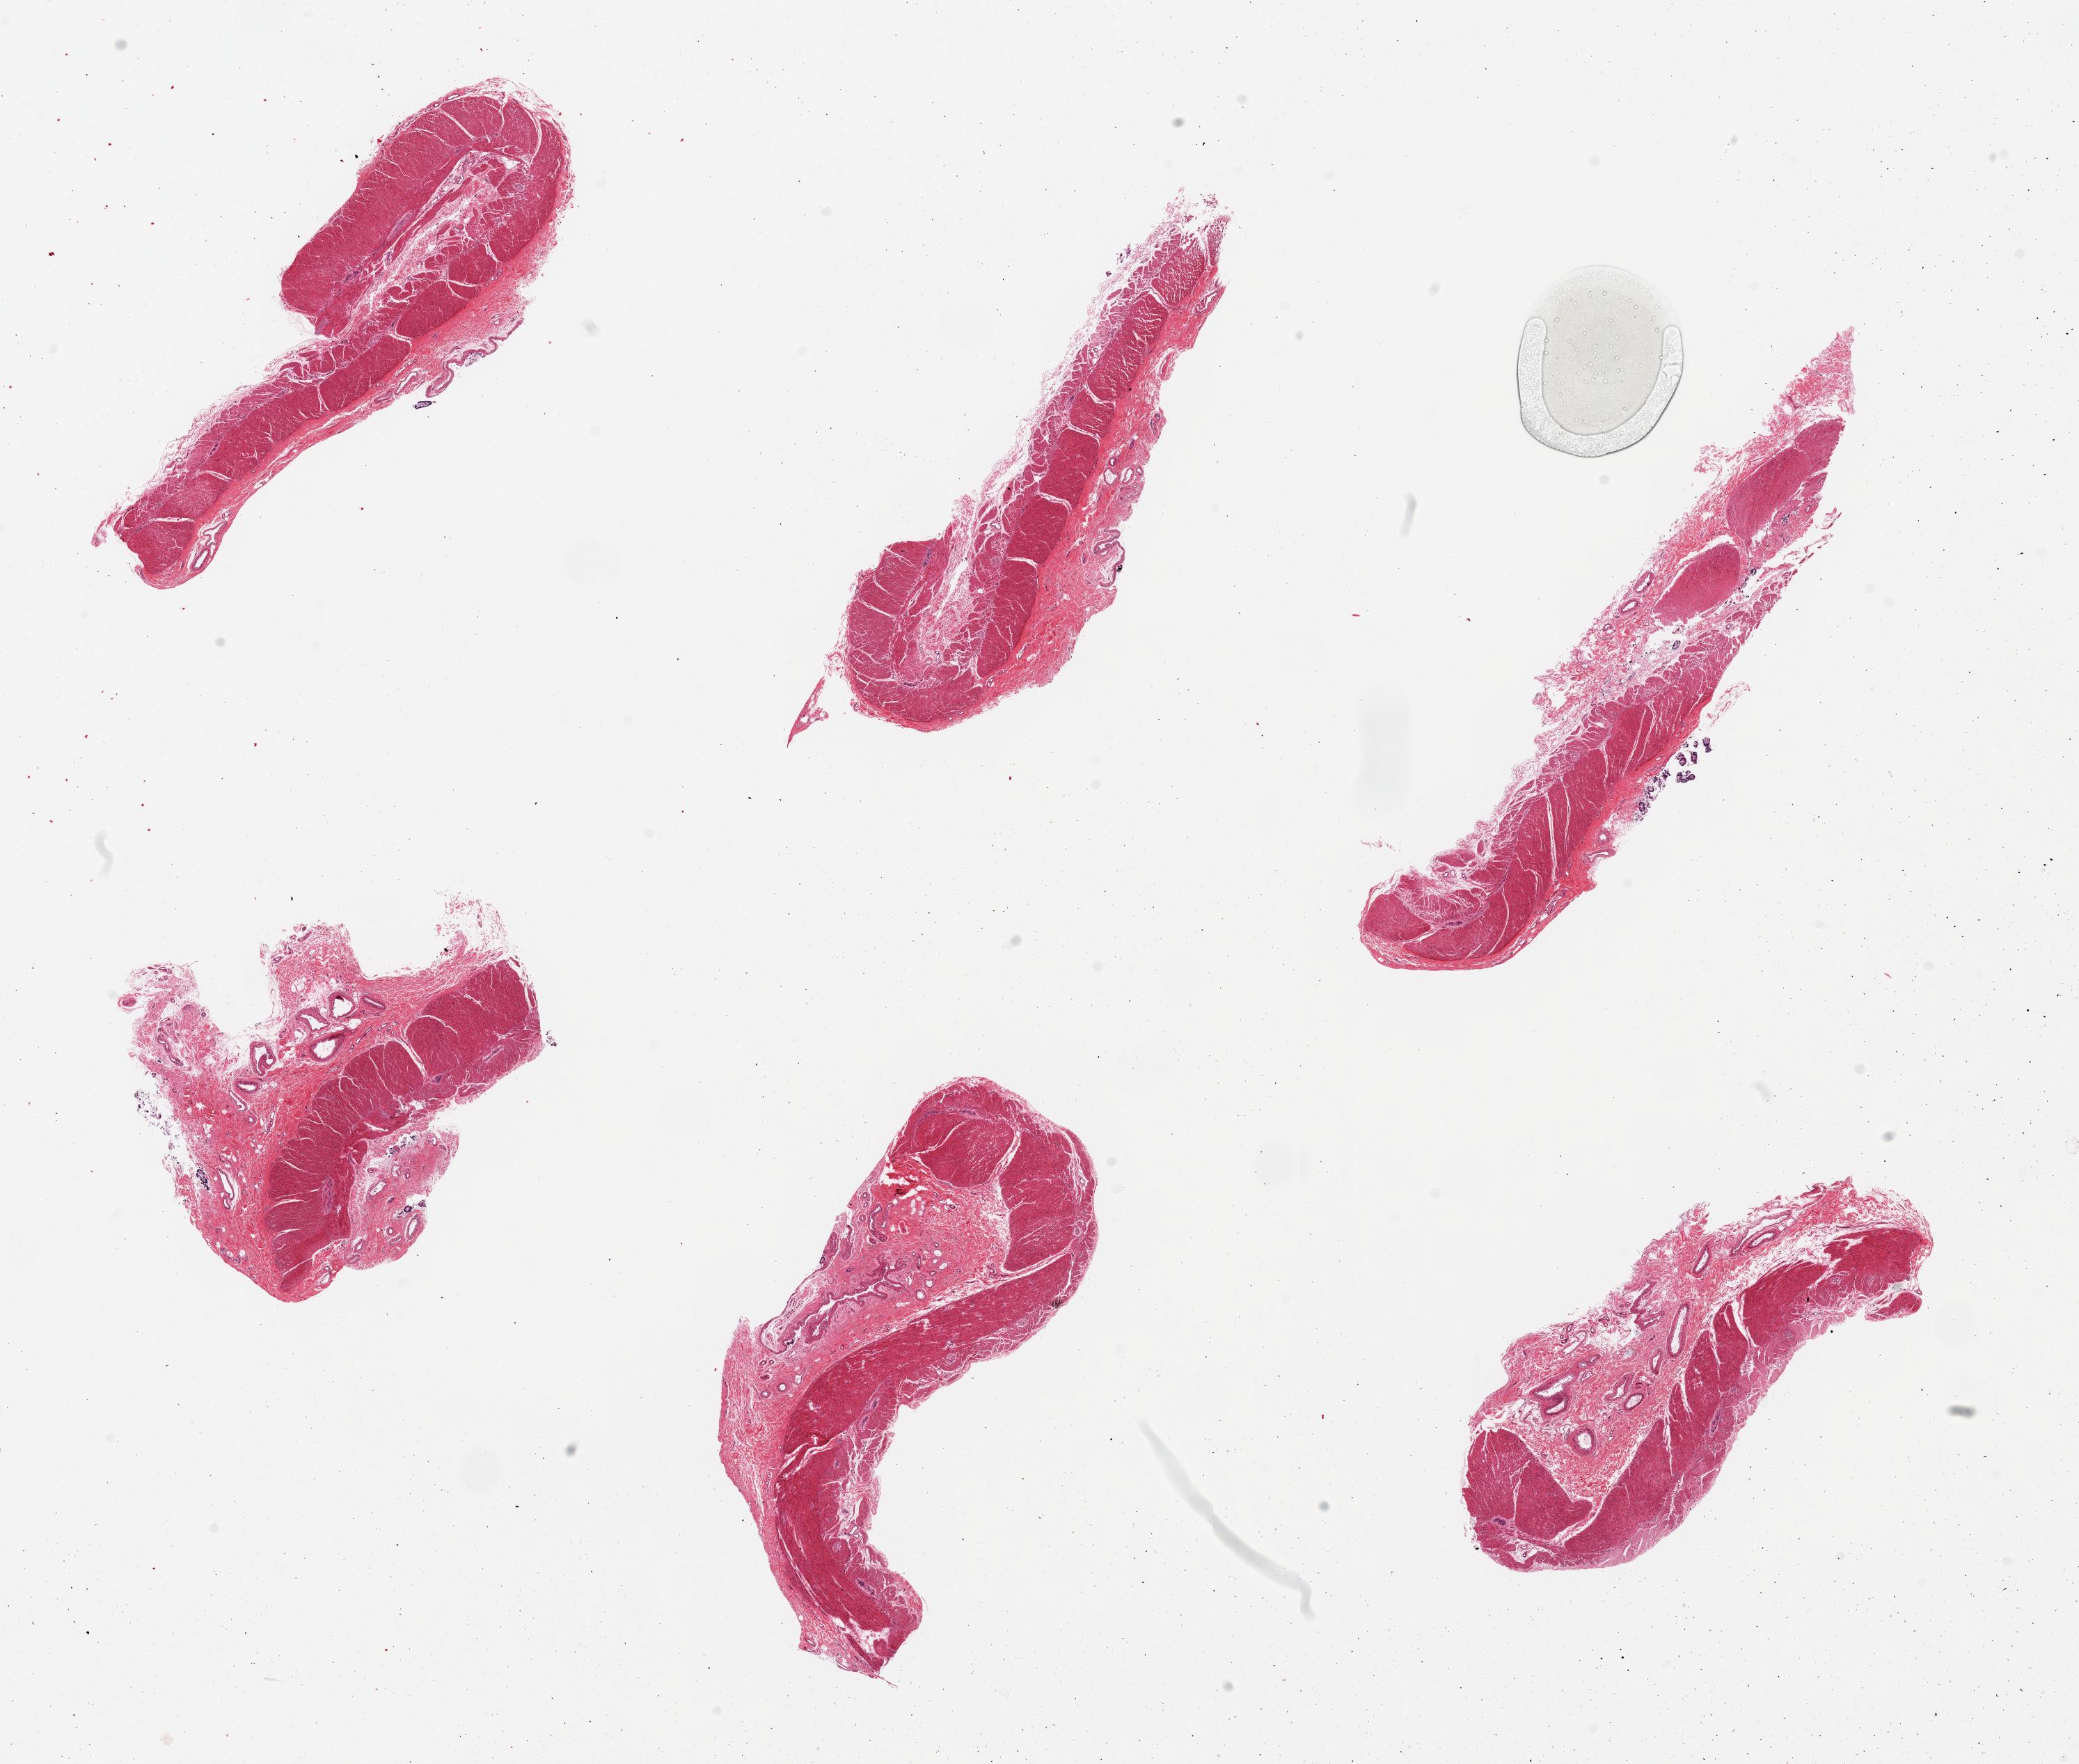
Hematoxylin and eosin (H&E) whole-slide image, brightfield — a low-resolution overview of the entire scanned area, about 23.6 x 20.0 mm; PAXgene-fixed, paraffin-embedded tissue; target tissue: transverse colon; tissue donor sample. Donor sex: female.
Pathologist's review note for this sample: 6 pieces, mucosa completely sloughed.